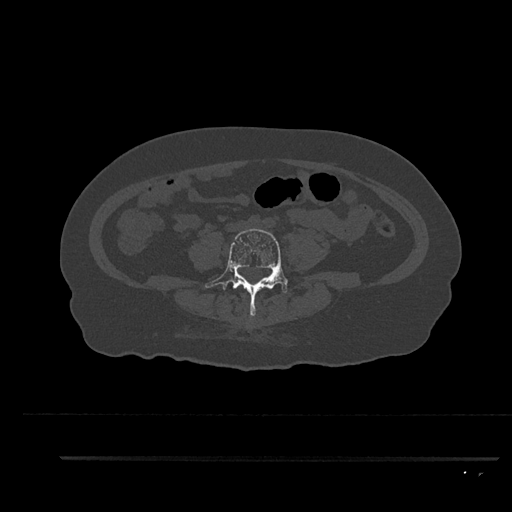
CT including the spine, one axial slice. Position 22 of 797 along the scan axis. Reconstruction kernel Br40s/3. 120 kVp. Bone window (W 1800 / L 400 HU). 0.5 mm slice thickness. 512 × 512 image matrix, field of view 408 × 408 mm. Patient: female, 44 years. From the clinical record (not read from this slice): primary cancer: renal; vertebrae with lytic lesions (as recorded): L1.
Structures marked on this image (semi-automatically segmented with operator editing):
- L4 vertebra: bounding box (x1, y1, x2, y2) in pixels: (205, 228, 288, 316)